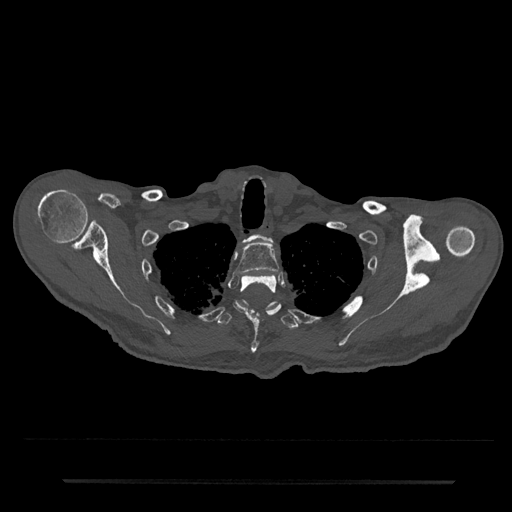
CT including the spine, one axial slice. Position 659 of 797 along the scan axis. Bone window (W 1800 / L 400 HU). 0.5 mm slice thickness. 512 × 512 image matrix, field of view 427 × 427 mm. Male patient, age 74 years. From the clinical record (not read from this slice): primary cancer: prostate.
Outlined on this slice (semi-automatically segmented with operator editing):
- T1 vertebra: bounding box [x1, y1, x2, y2] px = [244, 234, 273, 243]
- T2 vertebra: [236, 242, 279, 275]
- T3 vertebra: [234, 275, 281, 353]
- T4 vertebra: [216, 300, 299, 329]